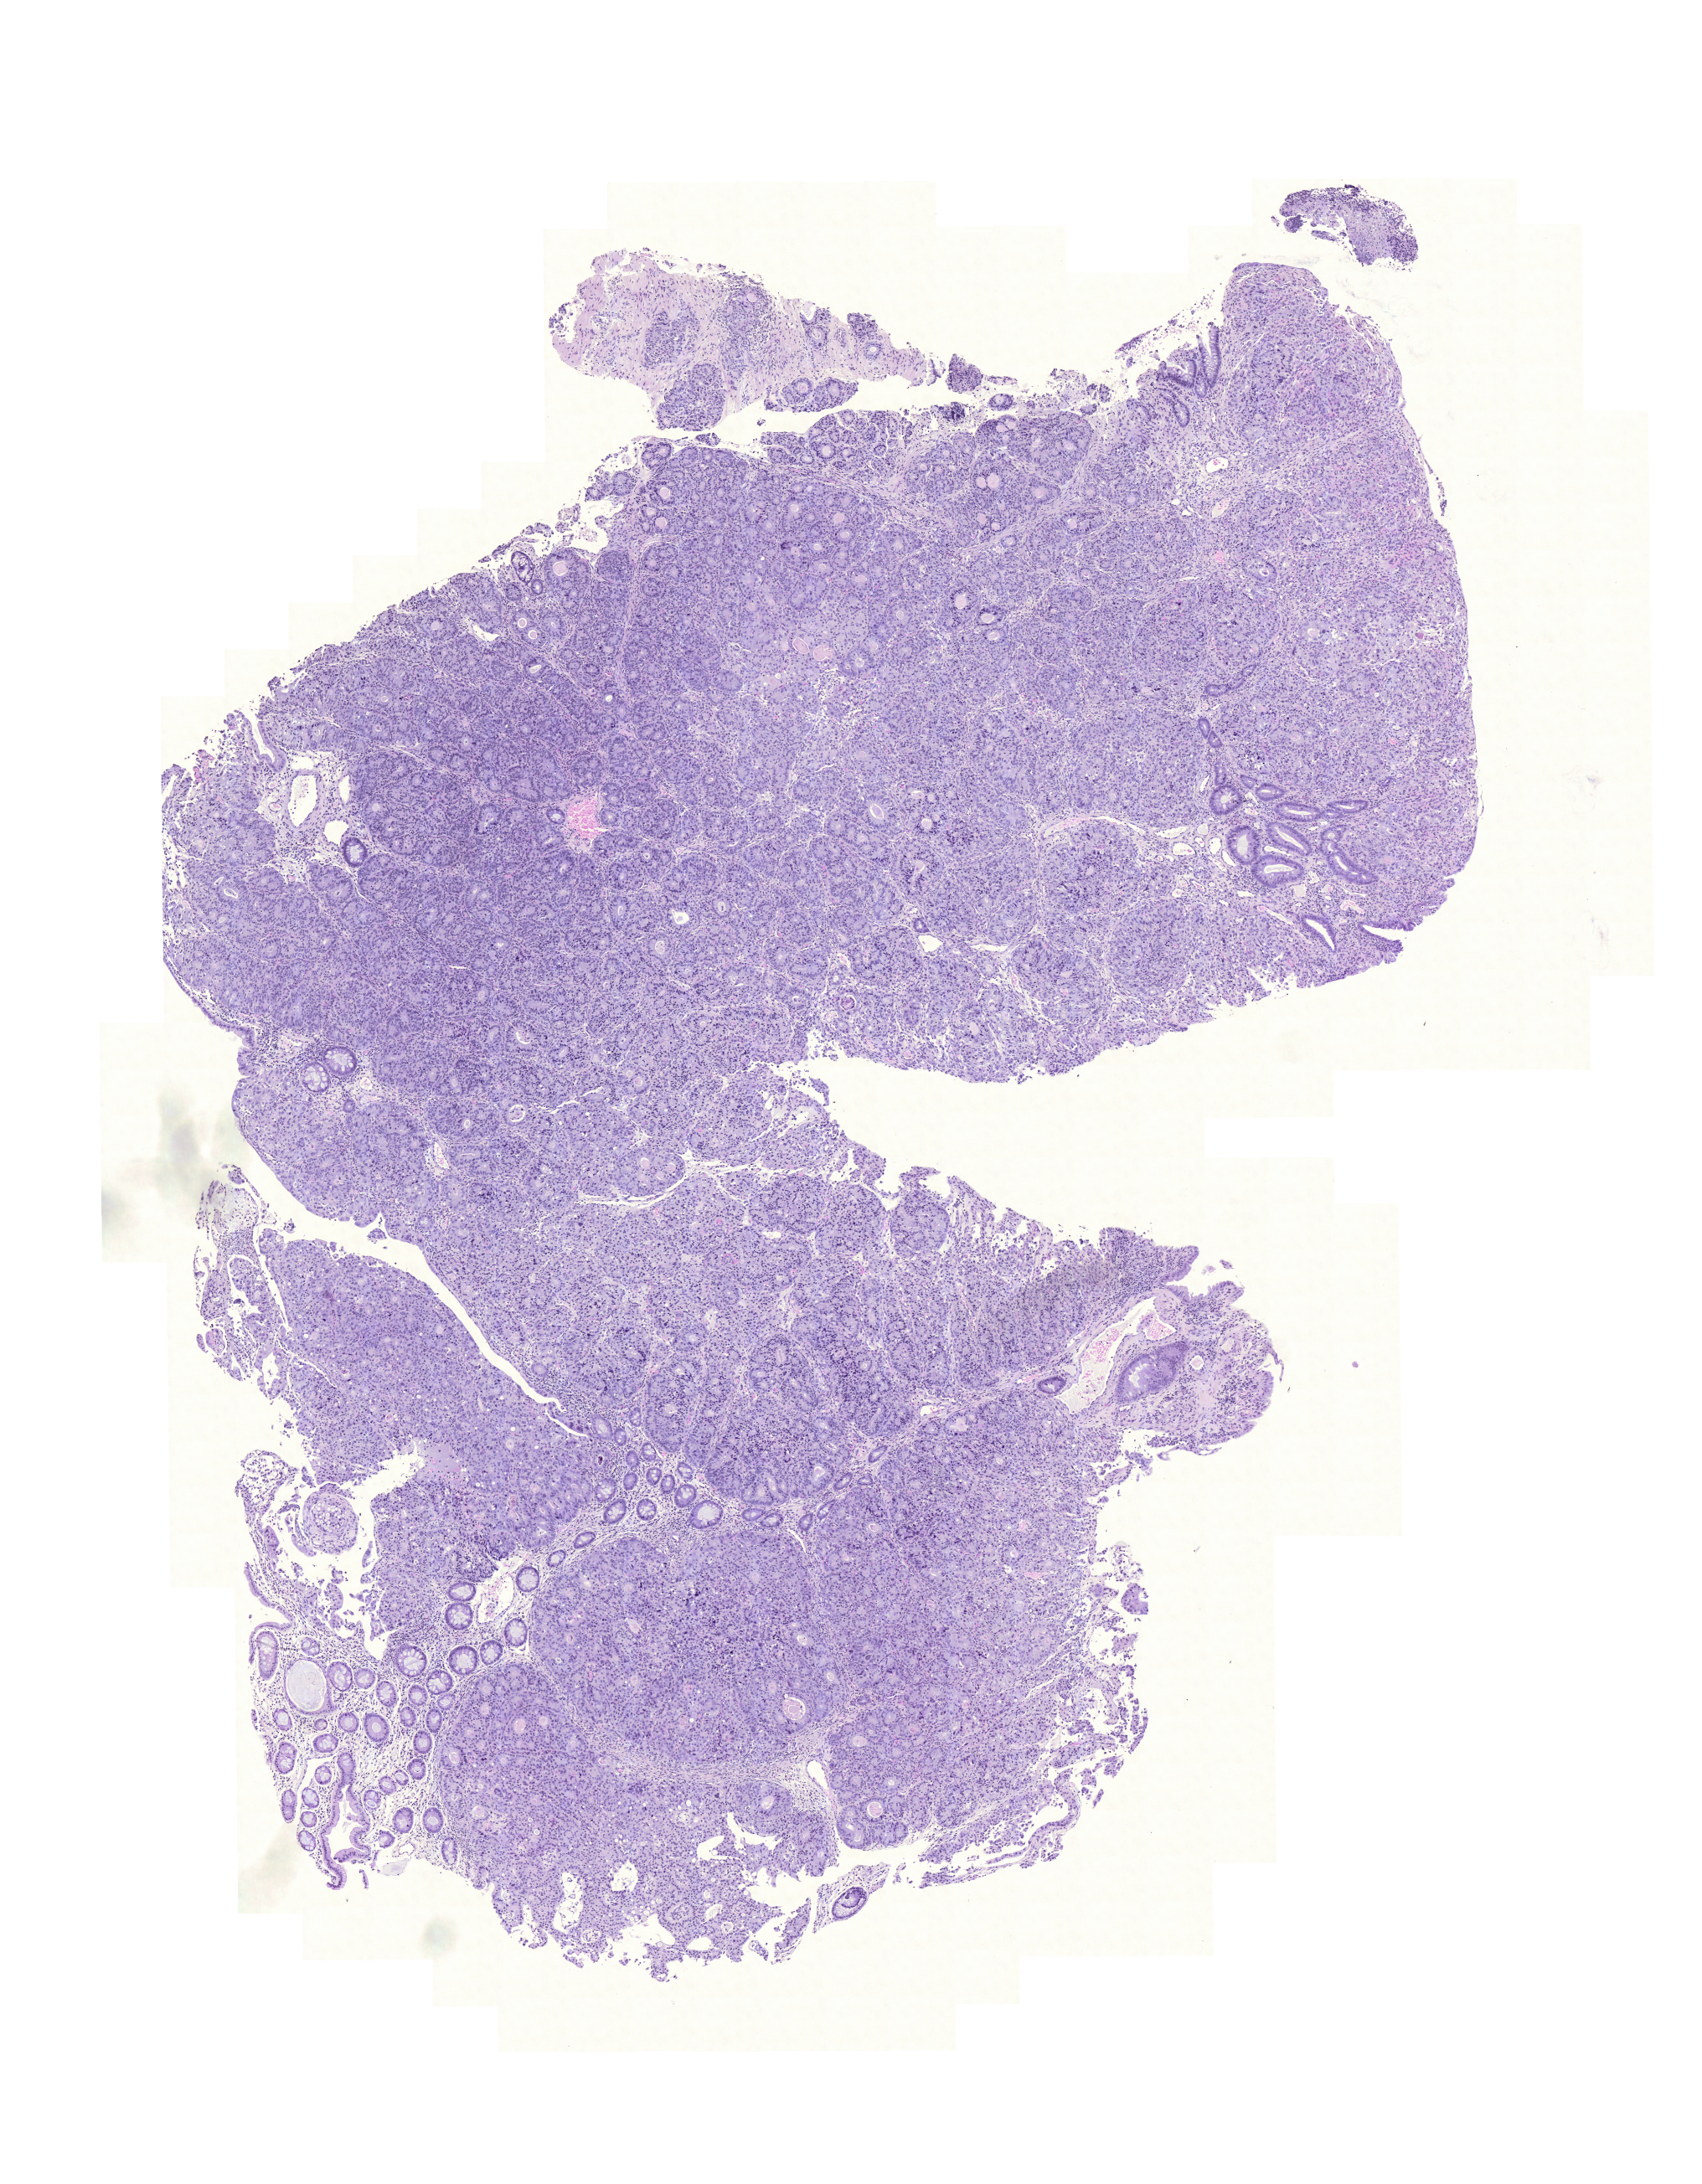
H&E whole-slide image, a low-resolution overview of the entire scanned area, about 7.6 x 9.7 mm; FFPE section; primary tumour sample from the colon. Patient: female, age at initial diagnosis 83 years.
AJCC pathologic stage: IIIC (6th edition). Diagnosis: Adenocarcinoma, NOS (sigmoid colon). Lymph nodes positive (case pathology): 32 of 40 examined.